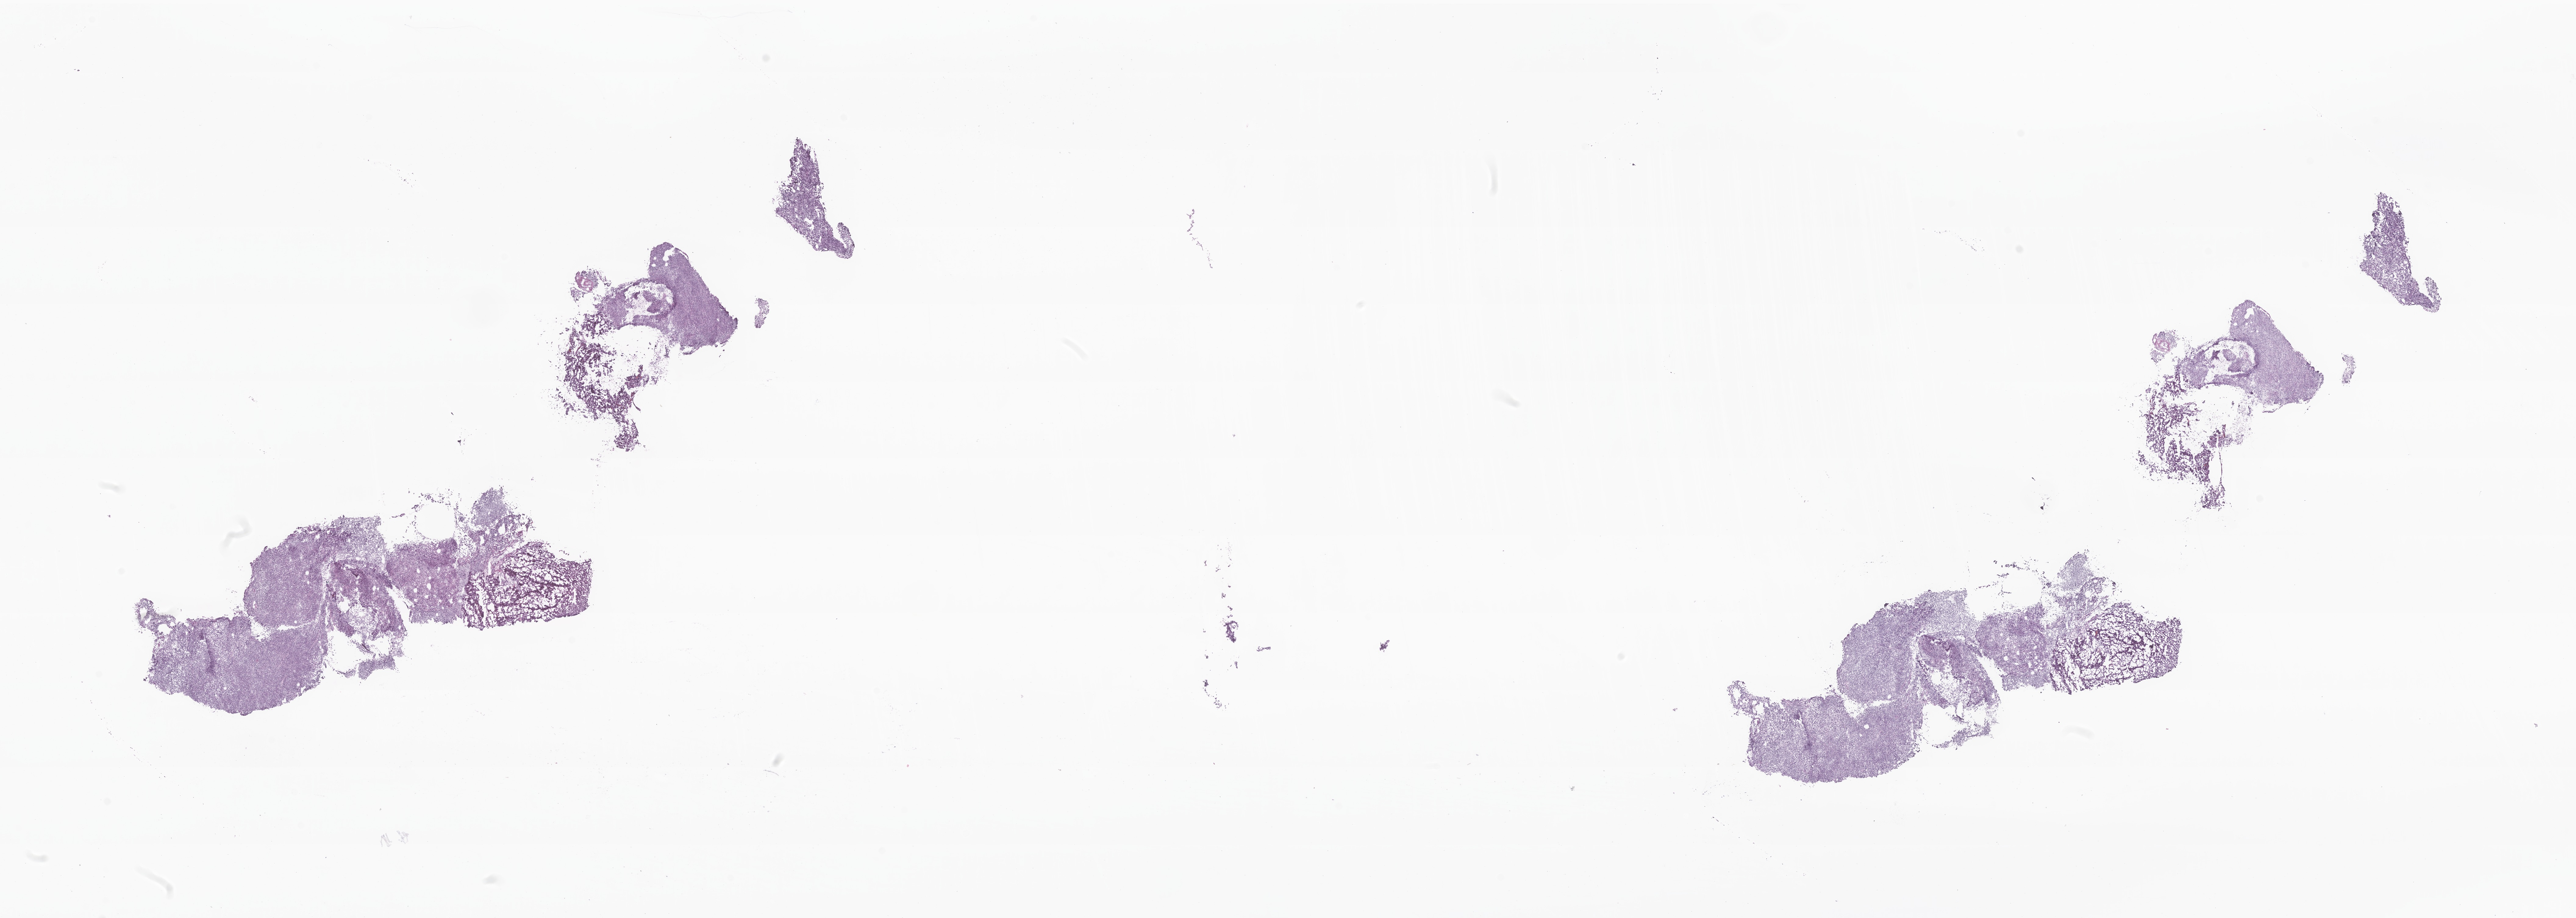
Whole-slide image, haematoxylin and eosin stain of tumor tissue from the brain — whole scanned area (about 35.6 x 12.7 mm) shown as a low-resolution overview; cryosection (OCT / tissue freezing medium). Patient female; age 472 days (about 1.3 years).
Diagnosis (ICD-O-3 morphology term): Medulloblastoma, NOS.